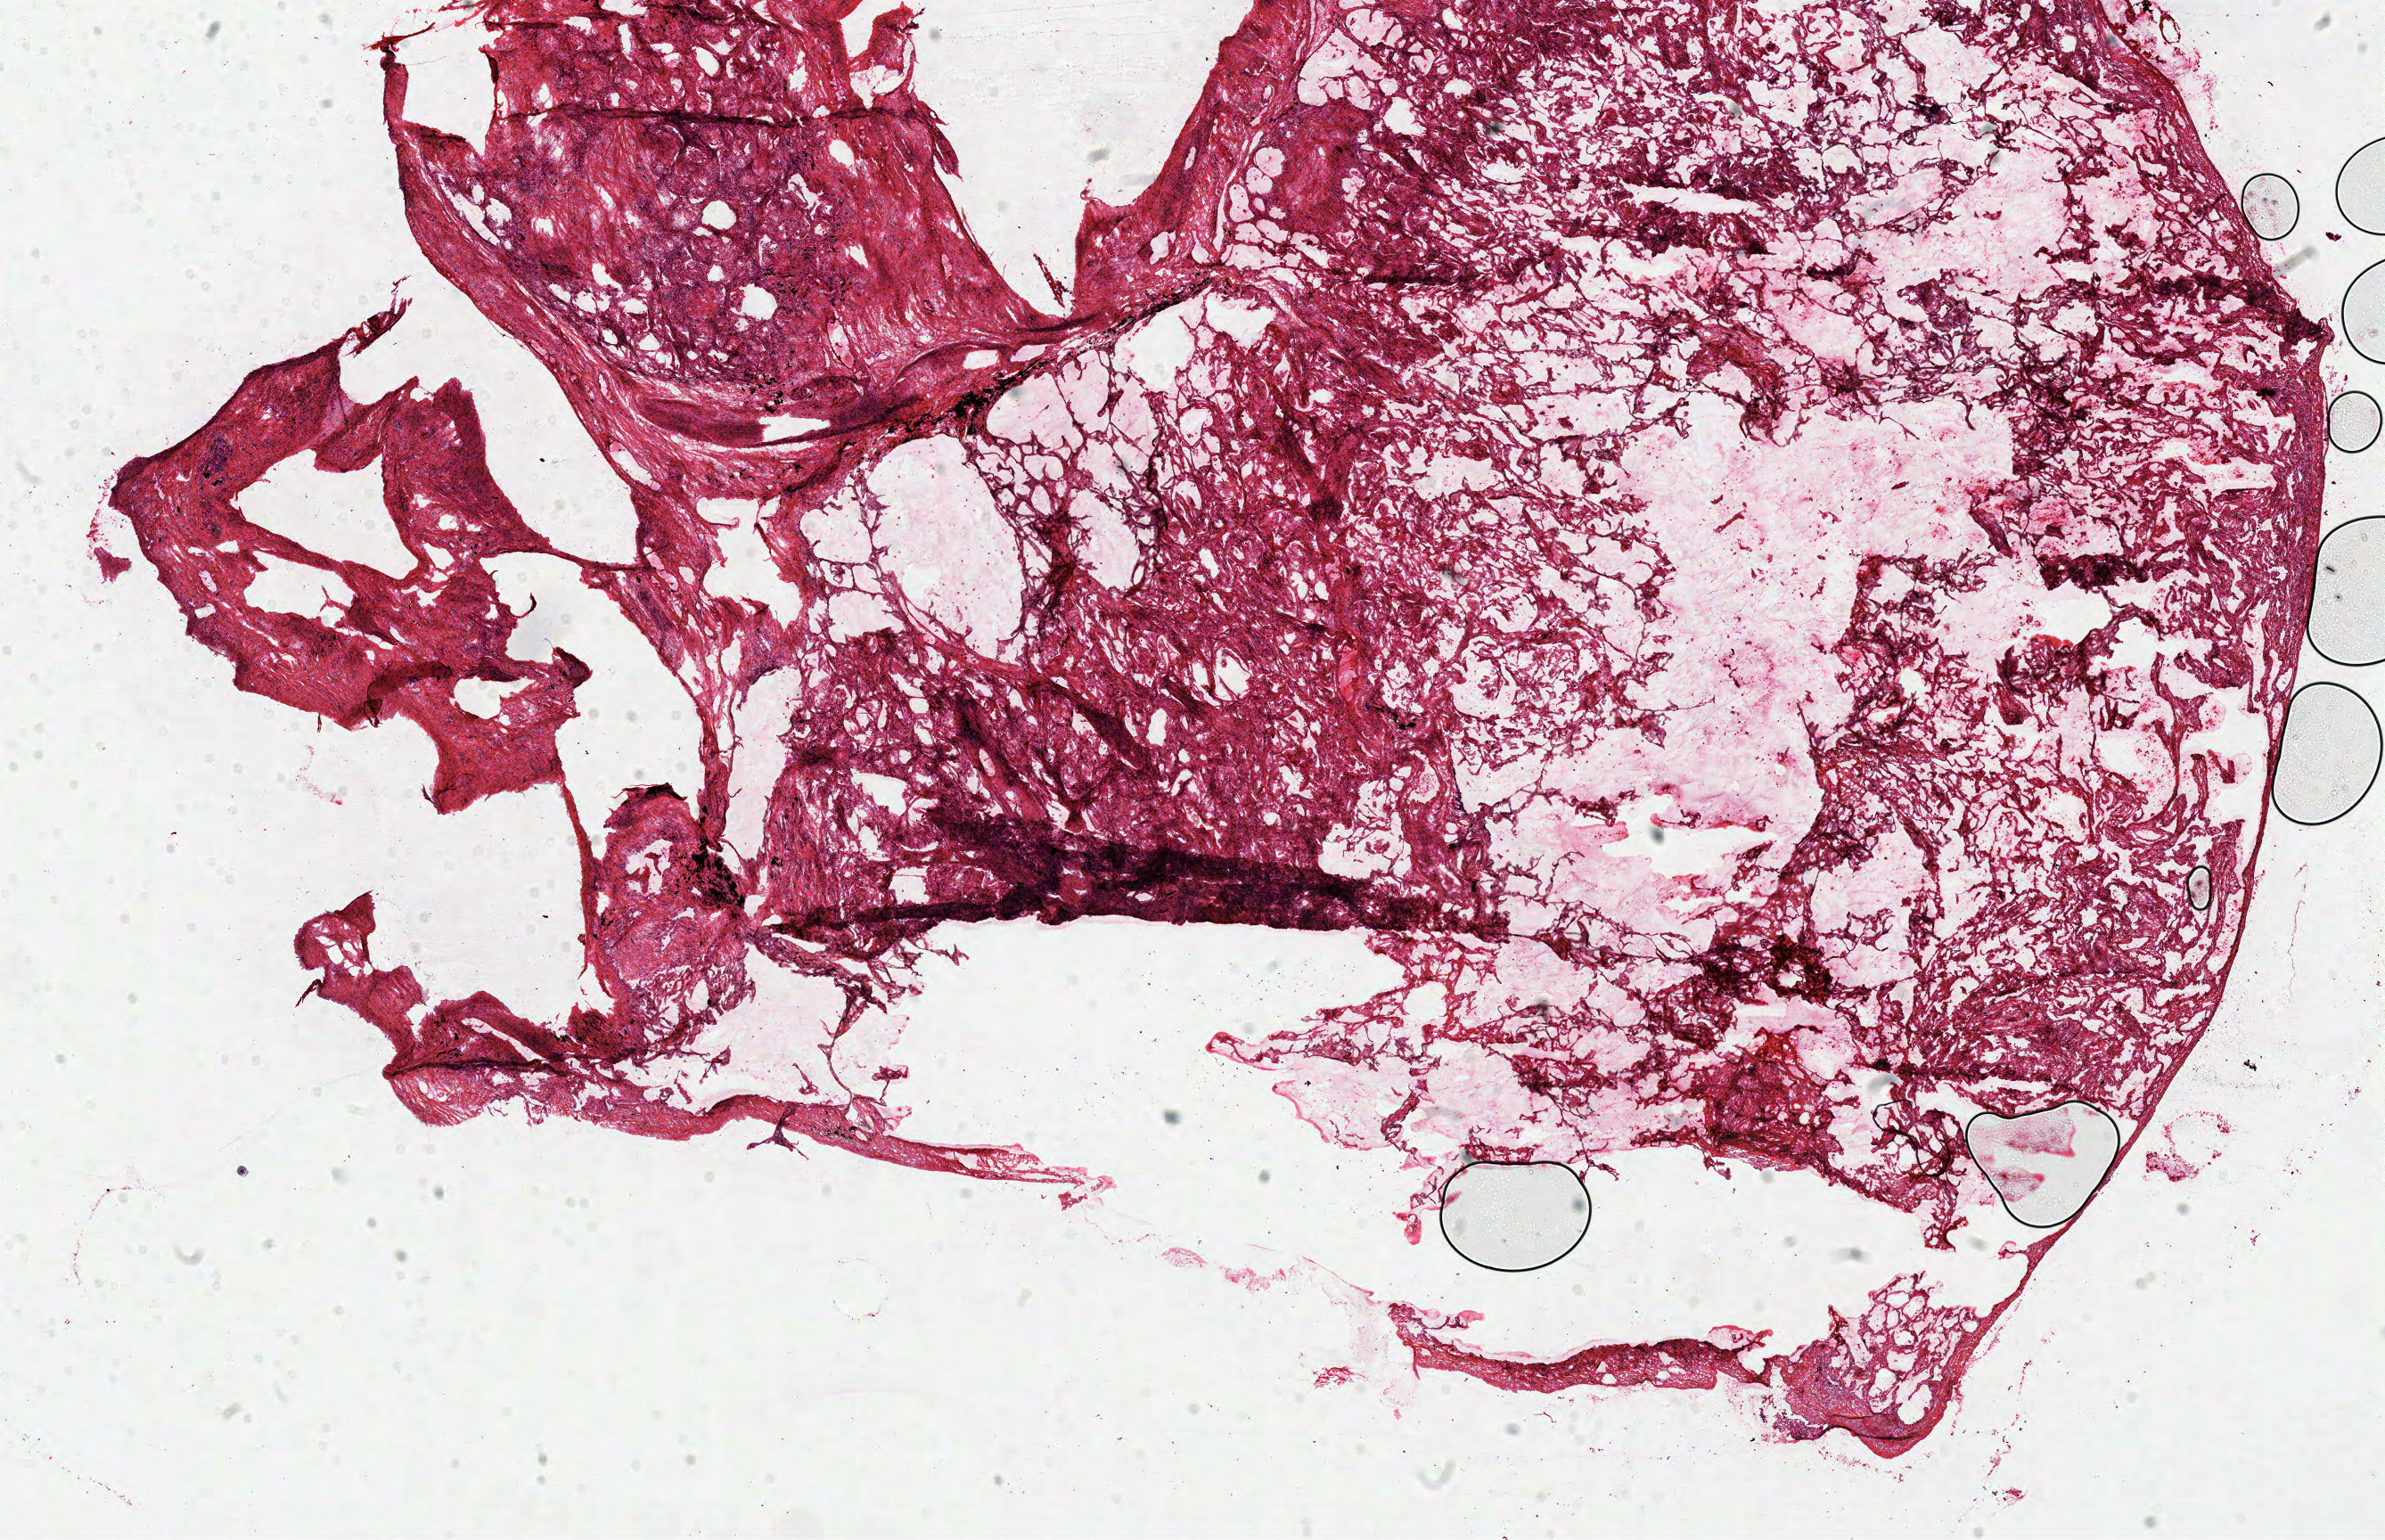
Whole-slide histology image, Hematoxylin and eosin (H&E) stained, shown as a low-resolution overview of the whole scanned area (about 21.0 x 13.6 mm), frozen section from the top of the tissue portion, sample: solid tissue normal (non-tumour tissue), lung. Male patient; age at initial diagnosis 85 years.
- this section: solid tissue normal (non-tumour) sample from the same patient
- patient diagnosis: Adenocarcinoma with mixed subtypes (upper lobe, lung)